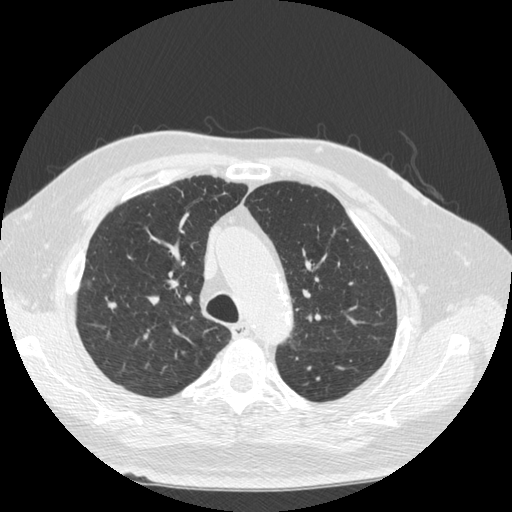
Axial slice from a low-dose chest CT screening exam; second annual screen; lung window (W 1500 / L -600 HU); 1.25 mm slice thickness; standard (soft-tissue) reconstruction kernel (STANDARD). Male, age 72 years at enrolment.
- Lesion marked by an expert reader, bounding box (x1, y1, x2, y2) in pixels: (87, 289, 123, 319).
- No non-calcified nodule or mass ≥4 mm was recorded by the screening reader at this exam.
- Official screen result: negative screen, minor abnormalities not suspicious for lung cancer.